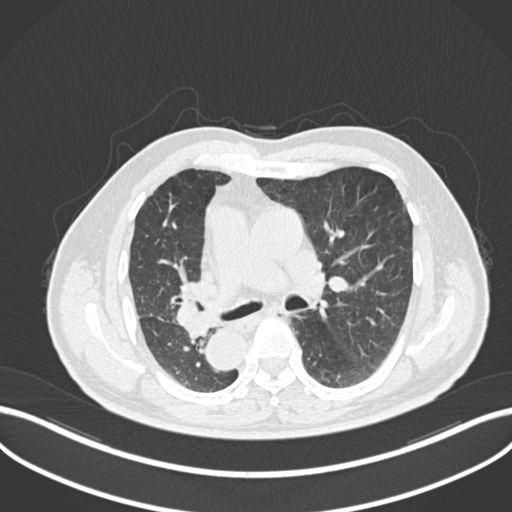
Chest CT, one axial slice; lung window (W 1500 / L -600 HU); 512 × 512 image matrix. Male patient, age 67 years. Case-level facts recorded for this patient, not image findings: clinical TNM (as recorded): T2a N0 M0.
Annotated regions visible in this slice (rectangle marked by the reading radiologist):
- lung tumour (recorded histology: squamous cell carcinoma): bounding box (x1, y1, x2, y2) in pixels: (172, 273, 228, 343)